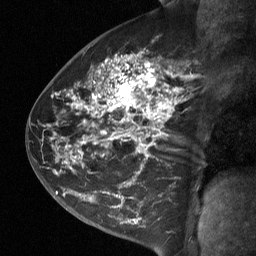
Breast MRI (dynamic contrast-enhanced), one sagittal slice; slice 40 of 64 in the series (ordered by position); dynamic contrast-enhanced study with each time point stored as its own series, time point 2 of 3 at this slice position (early post-contrast, ordered by acquisition time); 1.5 T; TE 4.8 ms, TR 27 ms; 256 × 256 image matrix, field of view 200 × 200 mm. Female patient, age 42 years. Case-level facts recorded for this patient, not image findings: setting: breast cancer imaged before/during neoadjuvant chemotherapy; receptor status: triple-negative.
Structures marked on this image (semi-automatic segmentation, software-assisted and operator-edited):
- analysis volume of interest (the breast-tissue region the enhancement analysis was run in; not a lesion): bounding box [x1, y1, x2, y2] px = [49, 45, 198, 197]
- tumour enhancement mask (voxels above the 90 % enhancement threshold inside the analysis volume of interest): [74, 55, 178, 162]